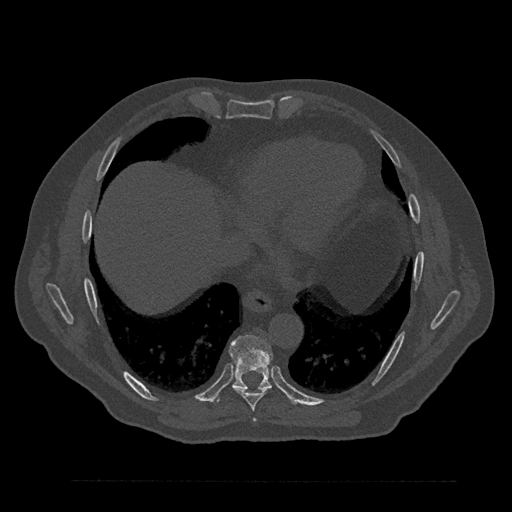
CT including the spine, one axial slice. Position 432 of 797 along the scan axis. Bone window (W 1800 / L 400 HU). 512 × 512 image matrix. Patient: male, 61 years. From the clinical record (not read from this slice): primary cancer: prostate.
Annotated regions visible in this slice (semi-automatic segmentation, software-assisted and operator-edited):
- T7 vertebra: box from (x=253, y=419) to (x=256, y=422) px
- T8 vertebra: (x=231, y=386)–(x=271, y=411)
- T9 vertebra: (x=217, y=334)–(x=272, y=401)